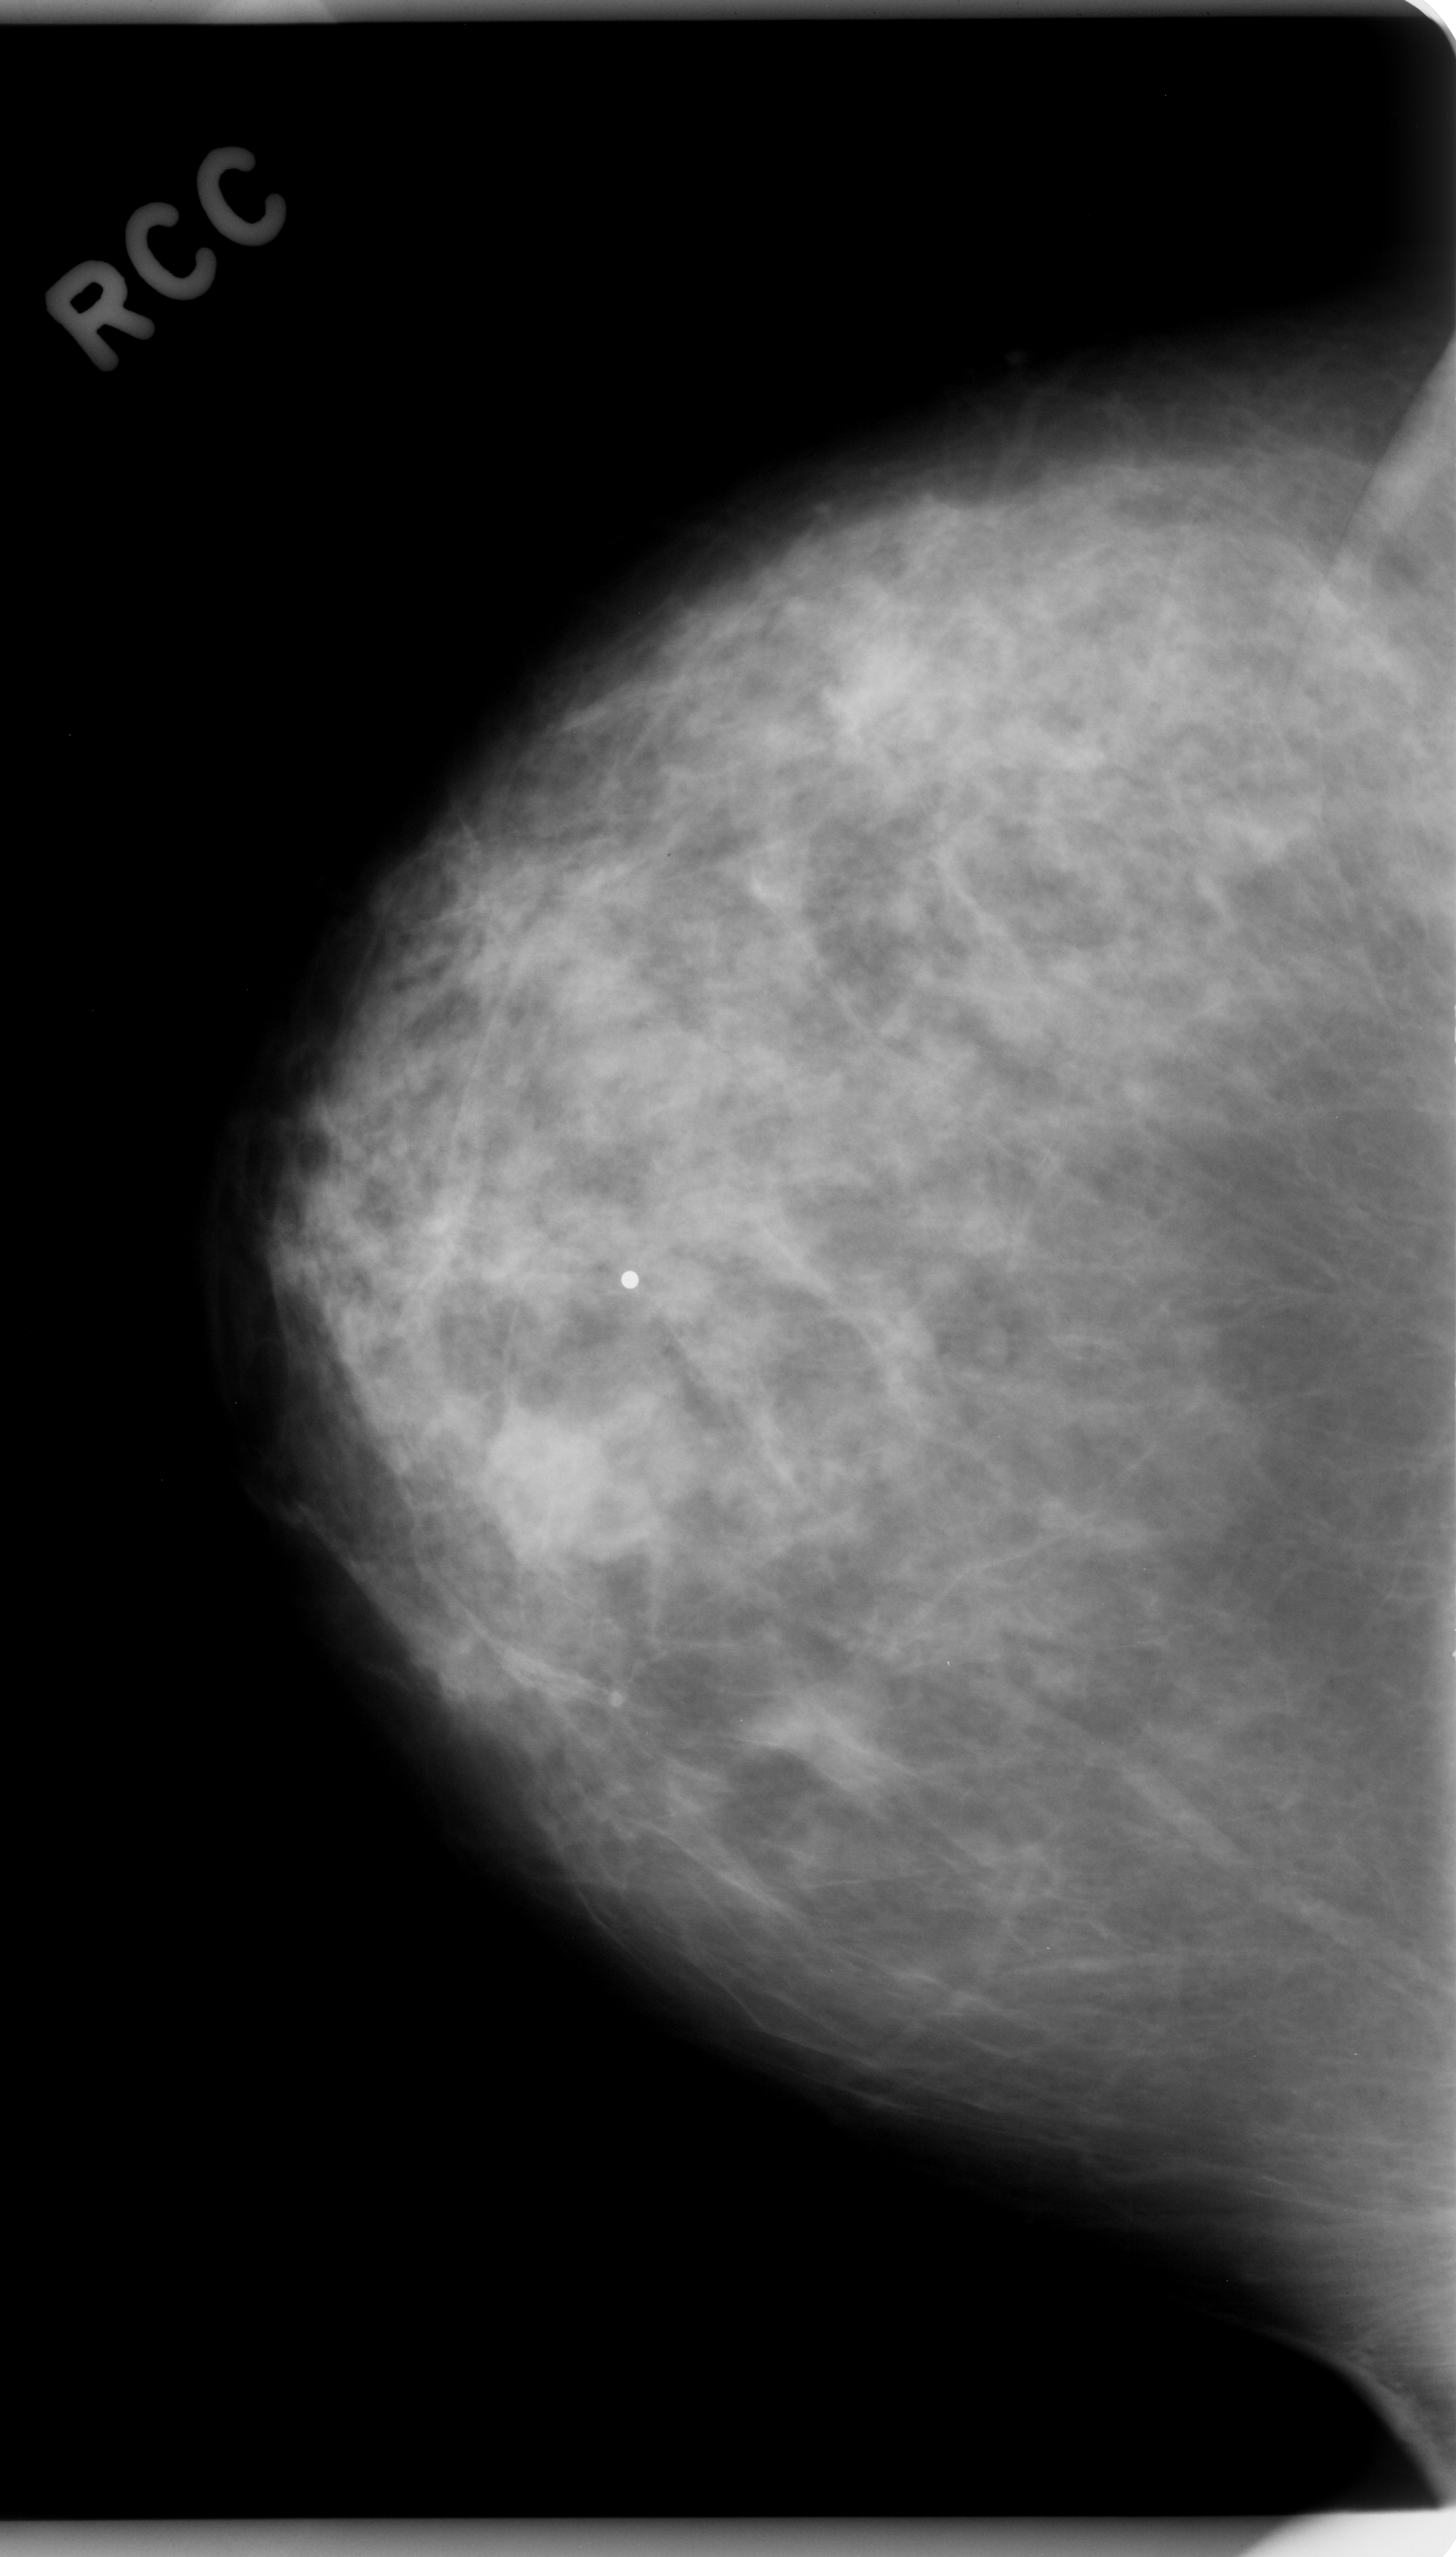
Mammogram (digitized film), right breast, craniocaudal (CC) view, breast composition: scattered fibroglandular densities (BI-RADS density category 2 of 4).
Abnormality record for this image: mass, shape oval, margins ill defined; BI-RADS assessment category 4; subtlety rating 4 on a 1 (subtle) to 5 (obvious) scale; pathology (as recorded): benign.